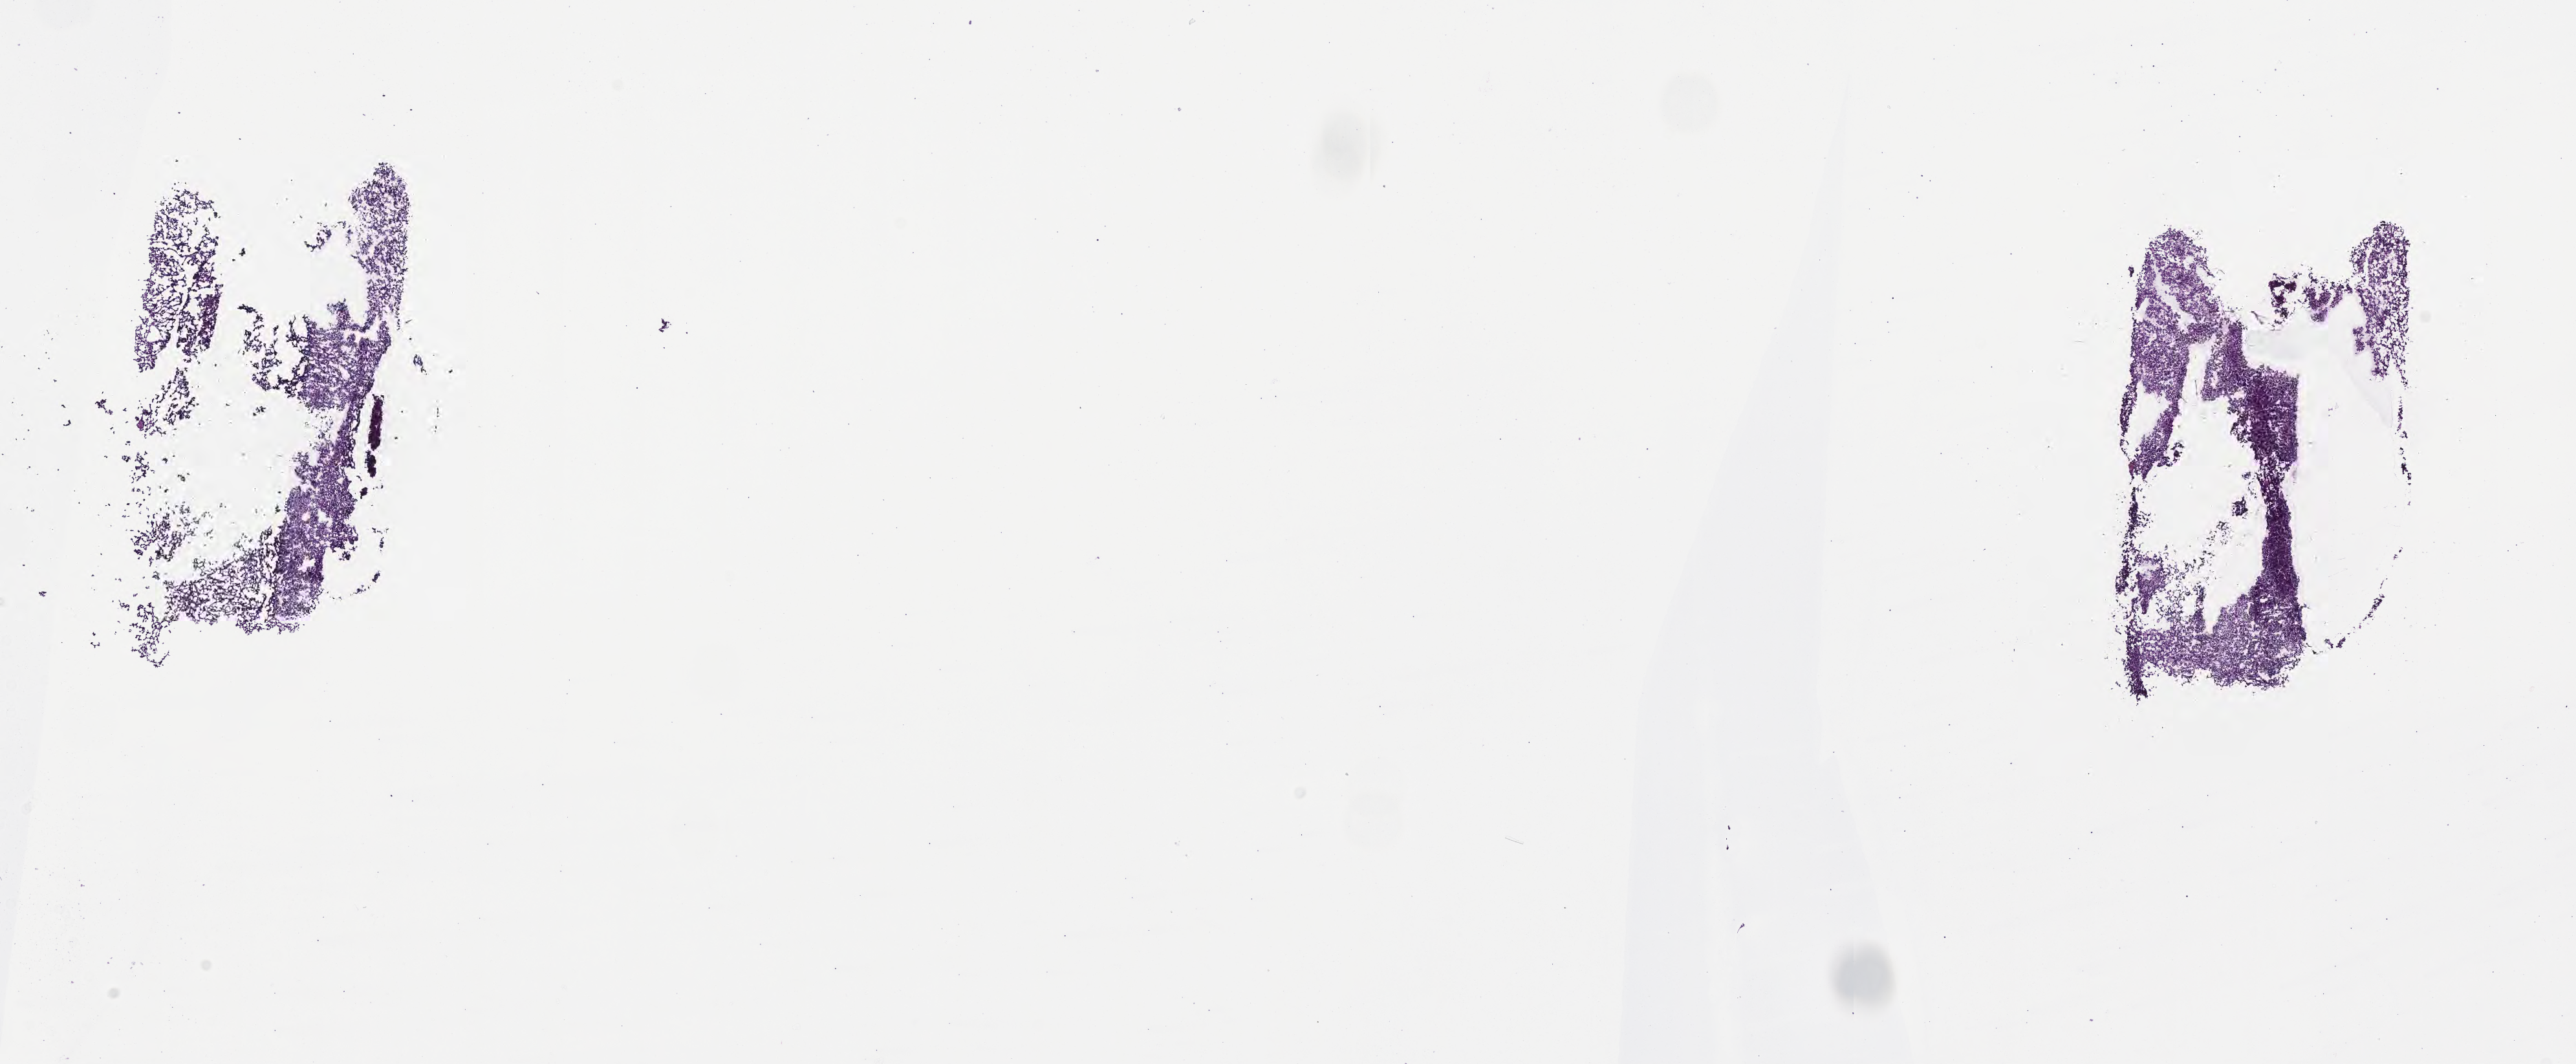
Hematoxylin and eosin (H&E) whole-slide image of tumor tissue from the brain — low-resolution overview of the scanned area, about 16.1 x 6.6 mm, frozen section. Male patient, age 37 months (3 years 1 month).
Recorded diagnosis: Medulloblastoma, NOS.